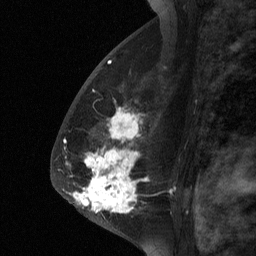
Breast MRI (dynamic contrast-enhanced), one sagittal slice; position 39 of 64 along the scan axis; dynamic contrast-enhanced study with each time point stored as its own series, time point 2 of 3 at this slice position (early post-contrast, ordered by acquisition time); 1.5 T; TE 4.8 ms, TR 27 ms; 256 × 256 image matrix, field of view 180 × 180 mm. Female patient, age 56 years. From the clinical record (not read from this slice): setting: breast cancer imaged before/during neoadjuvant chemotherapy; receptor status: HER2-positive.
Annotated regions visible in this slice (semi-automatic segmentation, software-assisted and operator-edited):
- analysis volume of interest (the breast-tissue region the enhancement analysis was run in; not a lesion): bounding box [x1, y1, x2, y2] px = [59, 104, 169, 229]
- tumour enhancement mask (voxels above the 90 % enhancement threshold inside the analysis volume of interest): [72, 117, 135, 213]